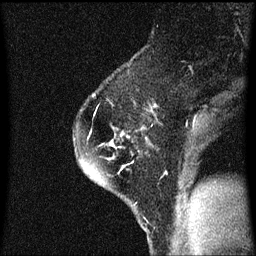
Breast MRI (dynamic contrast-enhanced), one sagittal slice. Position 44 of 60 along the scan axis. Dynamic contrast-enhanced series, image 2 of 3 at this slice position (ordered by acquisition). 1.5 T. TE 4.2 ms, TR 8.4 ms. 256 × 256 image matrix, field of view 200 × 200 mm. Patient: female, 60 years.
Structures marked on this image (semi-automatic segmentation, software-assisted and operator-edited):
- analysis volume of interest (the breast-tissue region the enhancement analysis was run in; not a lesion): box from (x=74, y=70) to (x=145, y=189) px
- tumour enhancement mask (voxels above the 70 % enhancement threshold inside the analysis volume of interest): (x=110, y=142)–(x=115, y=147)